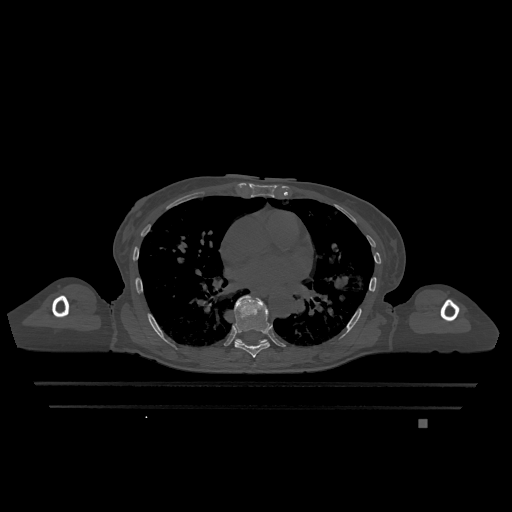
CT including the spine, one axial slice; position 728 of 1317 along the scan axis; bone window (W 1800 / L 400 HU); 0.5 mm slice thickness; 512 × 512 image matrix, field of view 500 × 500 mm. Patient: female, 74 years. Case-level facts recorded for this patient, not image findings: primary cancer: lung.
Structures marked on this image (semi-automatic segmentation, software-assisted and operator-edited):
- T7 vertebra: box from (x=234, y=296) to (x=270, y=358) px
- T9 vertebra: (x=236, y=339)–(x=268, y=345)